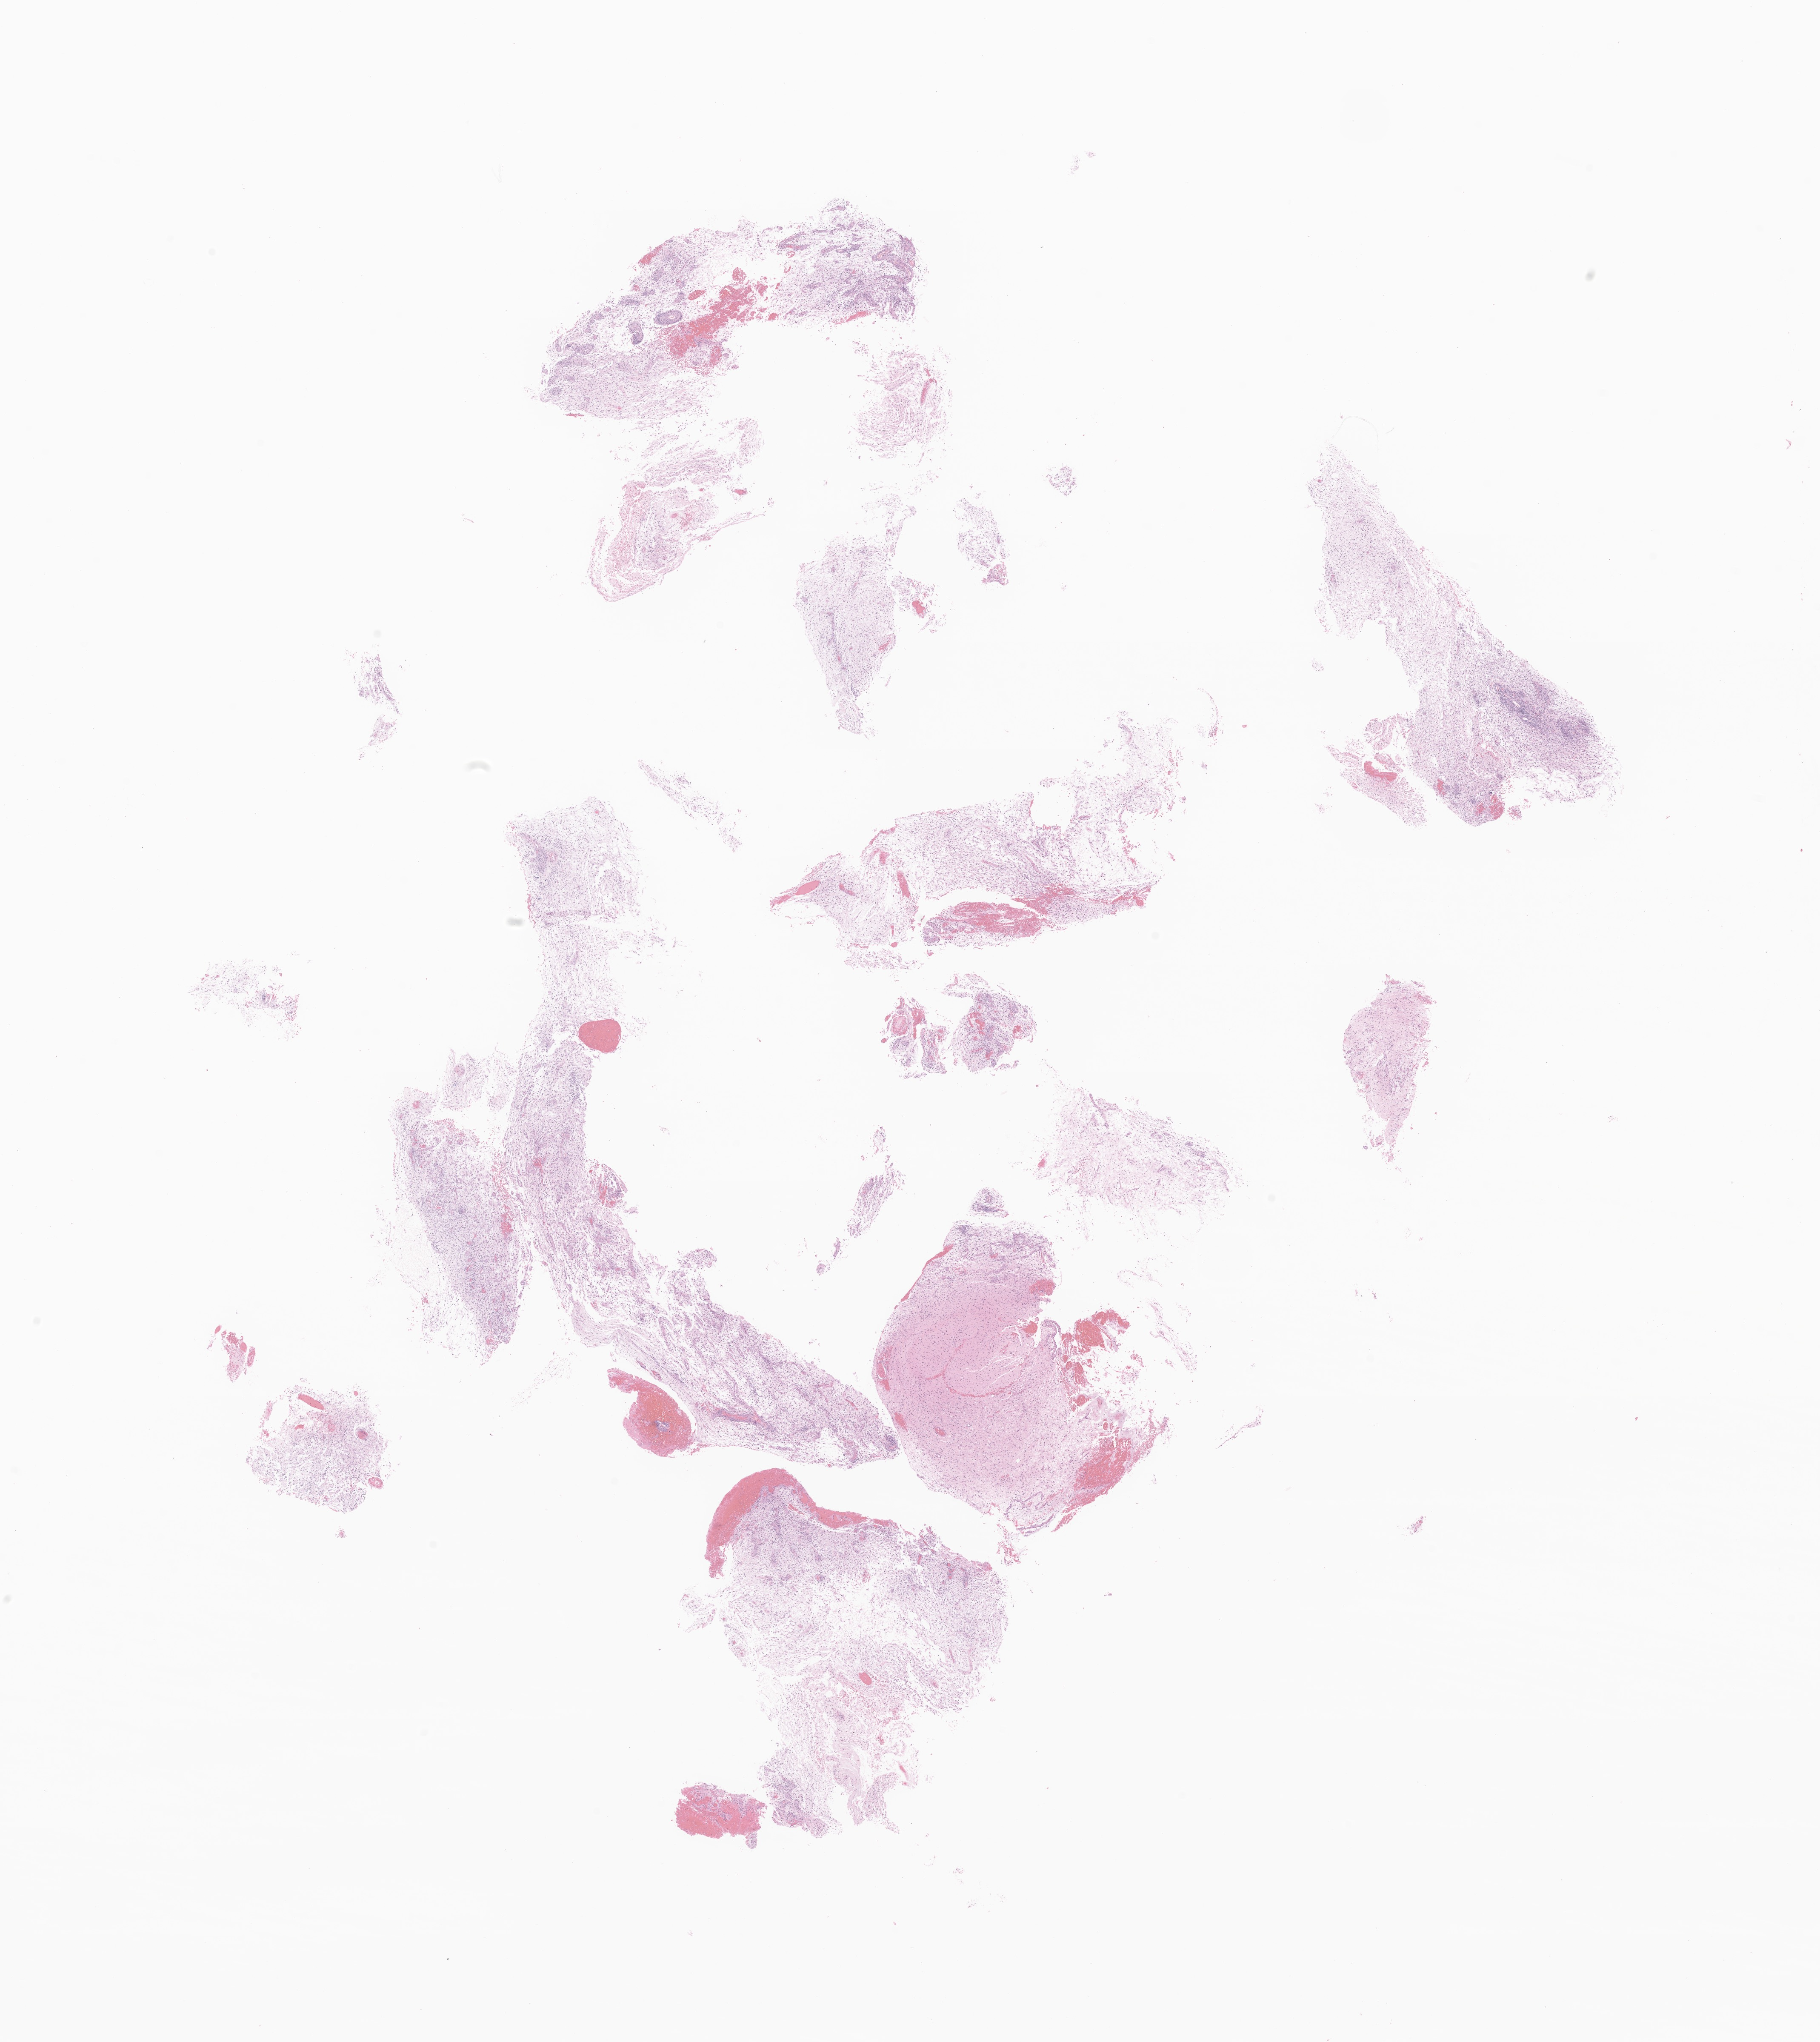
Digitized haematoxylin and eosin-stained section of tumor tissue from the frontal lobe — low-resolution overview of the scanned area, about 18.0 x 20.2 mm, FFPE section. Patient: male, age 191 months (15 years 11 months).
Recorded diagnosis: Glioma, malignant.